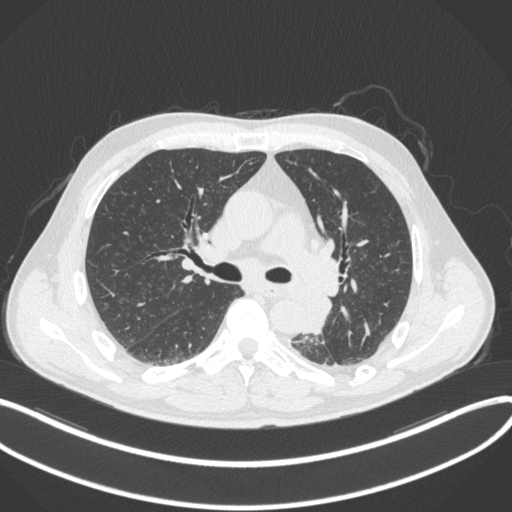
Chest CT, one axial slice. Slice 211 of 328 in the series (ordered by position). Reconstruction kernel B31f. Lung window (W 1500 / L -600 HU). 512 × 512 image matrix, field of view 400 × 400 mm. Male patient, age 59 years. Case-level facts recorded for this patient, not image findings: clinical TNM (as recorded): T2a N2 M0.
Structures marked on this image (rectangle marked by the reading radiologist):
- lung tumour (recorded histology: squamous cell carcinoma): bounding box <306,289,336,332> (left, top, right, bottom; pixels)